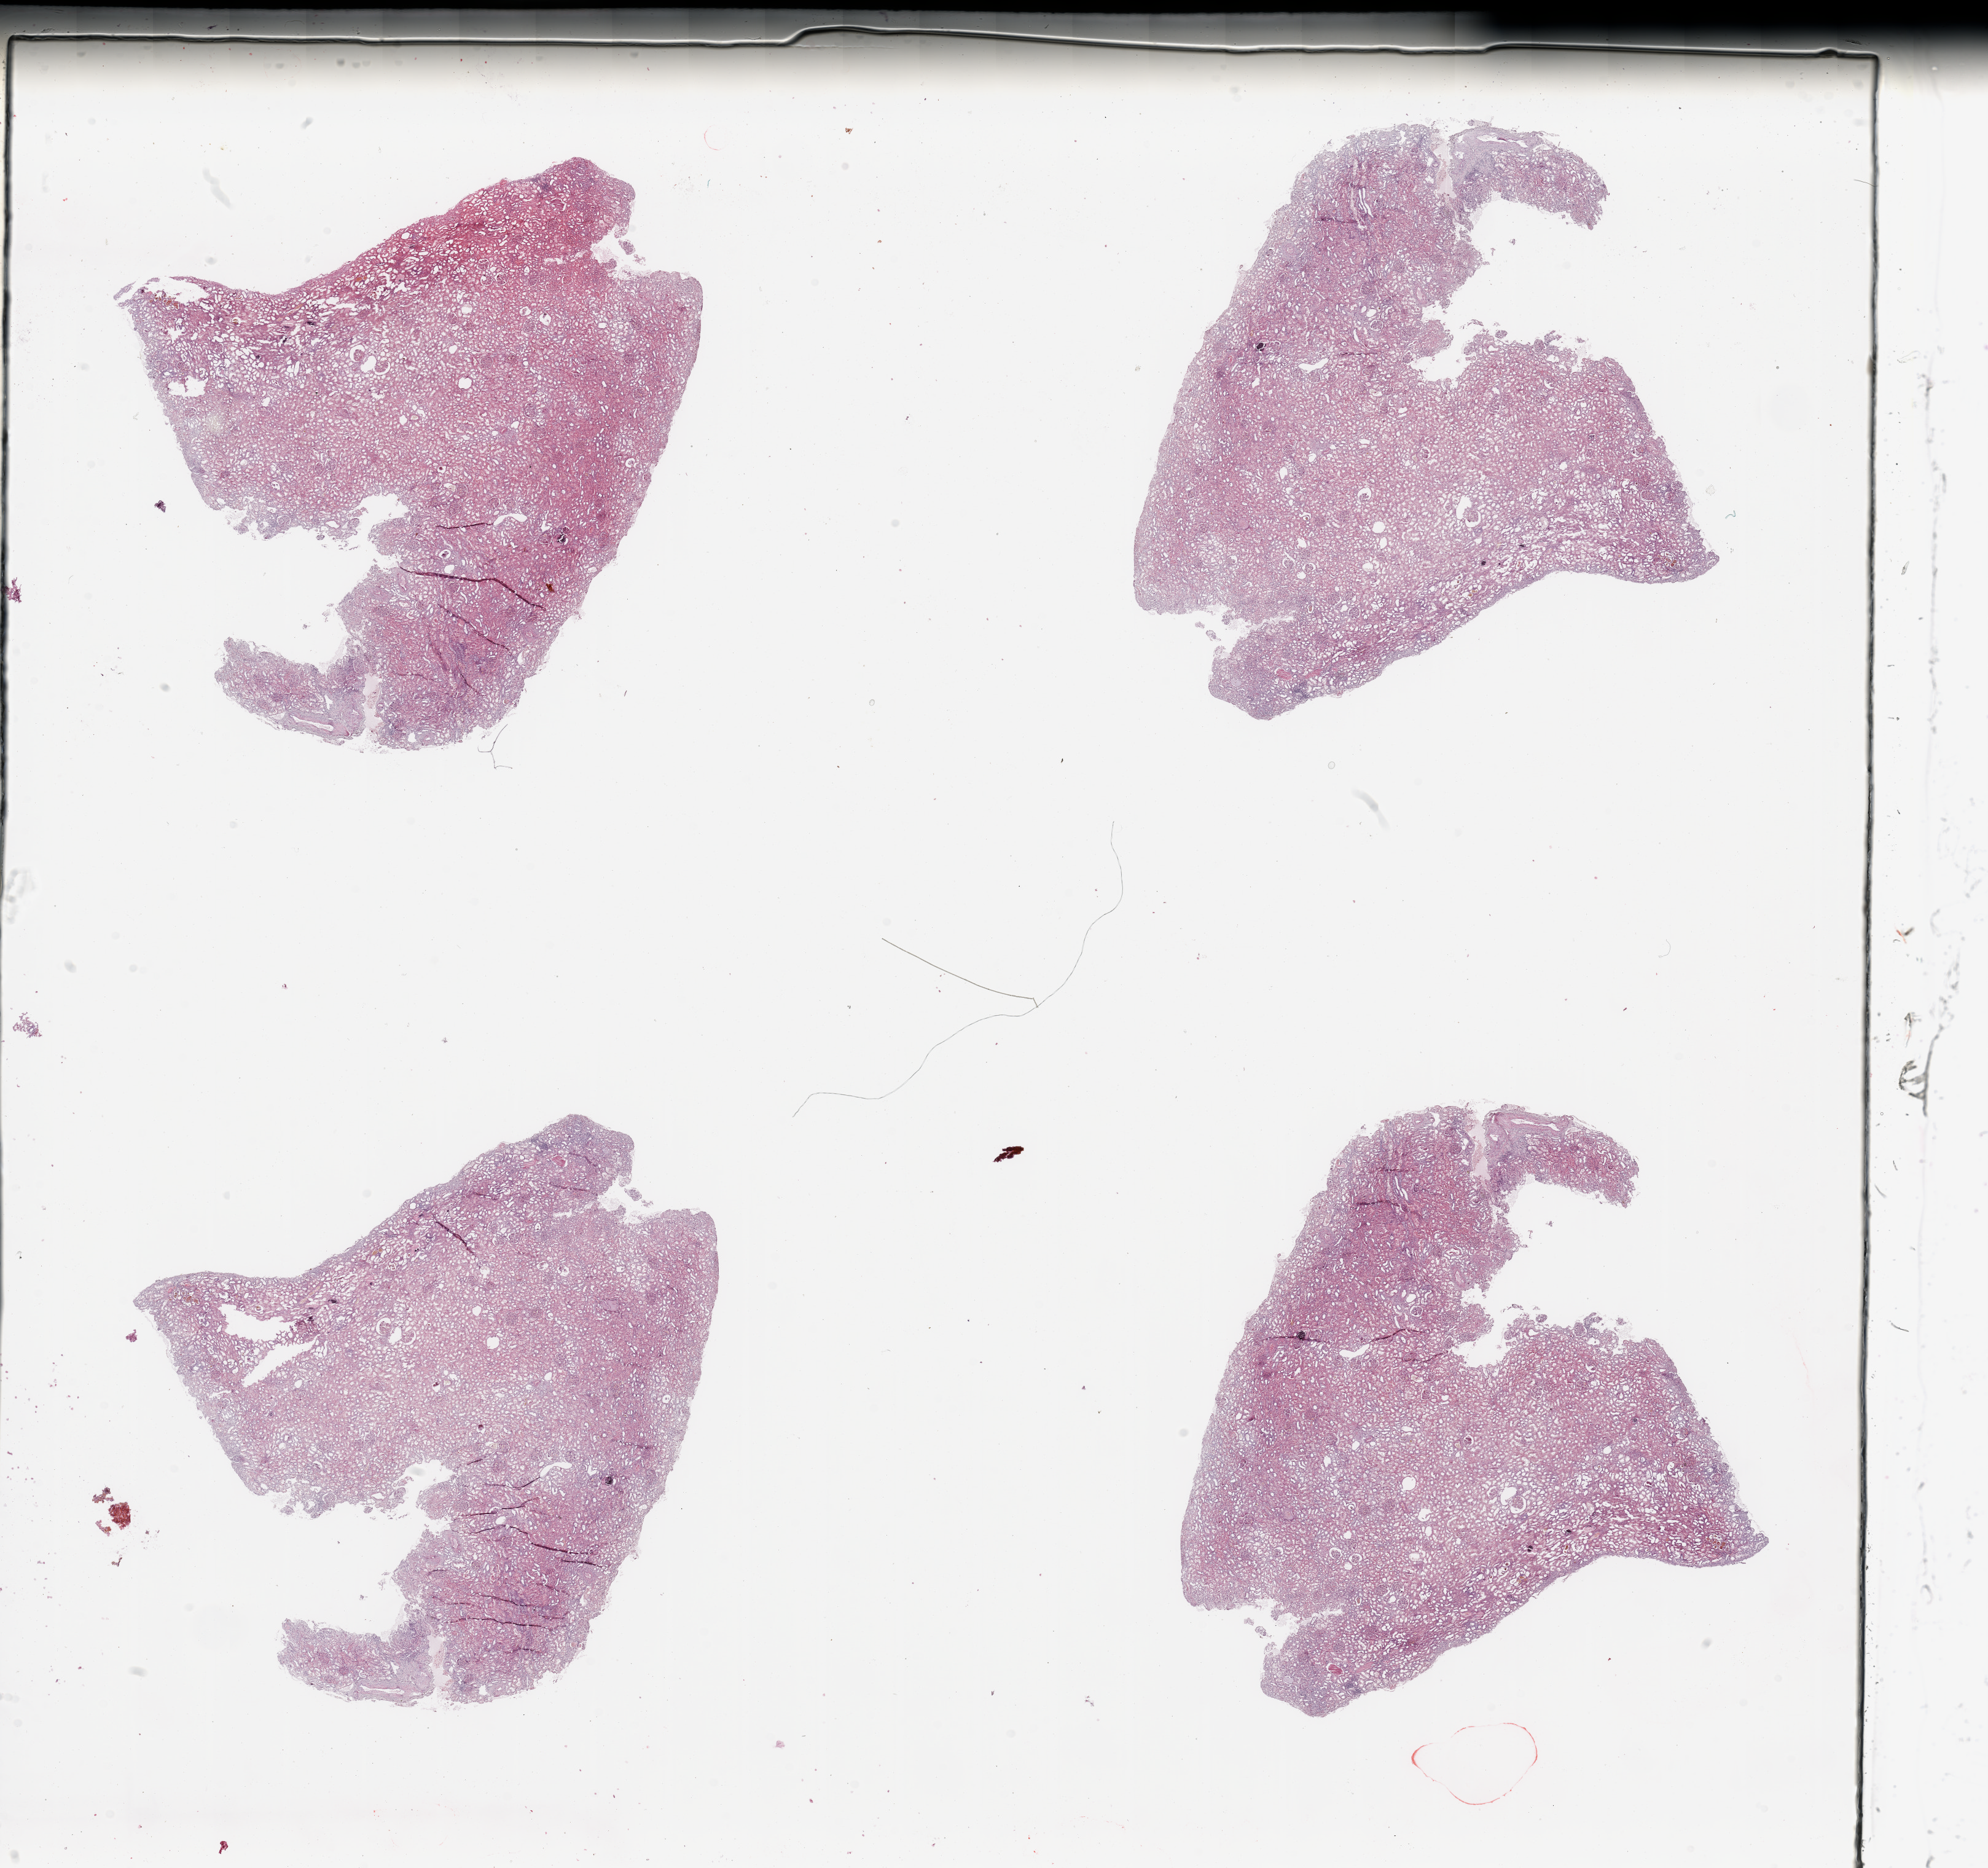
H&E-stained whole-slide image — shown as a low-resolution overview of the whole scanned area (about 25.6 x 24.0 mm). Normal (non-tumour) tissue sample, sampled site: kidney. 53-year-old male patient.
• this section: normal (non-tumour) tissue from the same patient
• patient diagnosis: Renal cell carcinoma, NOS